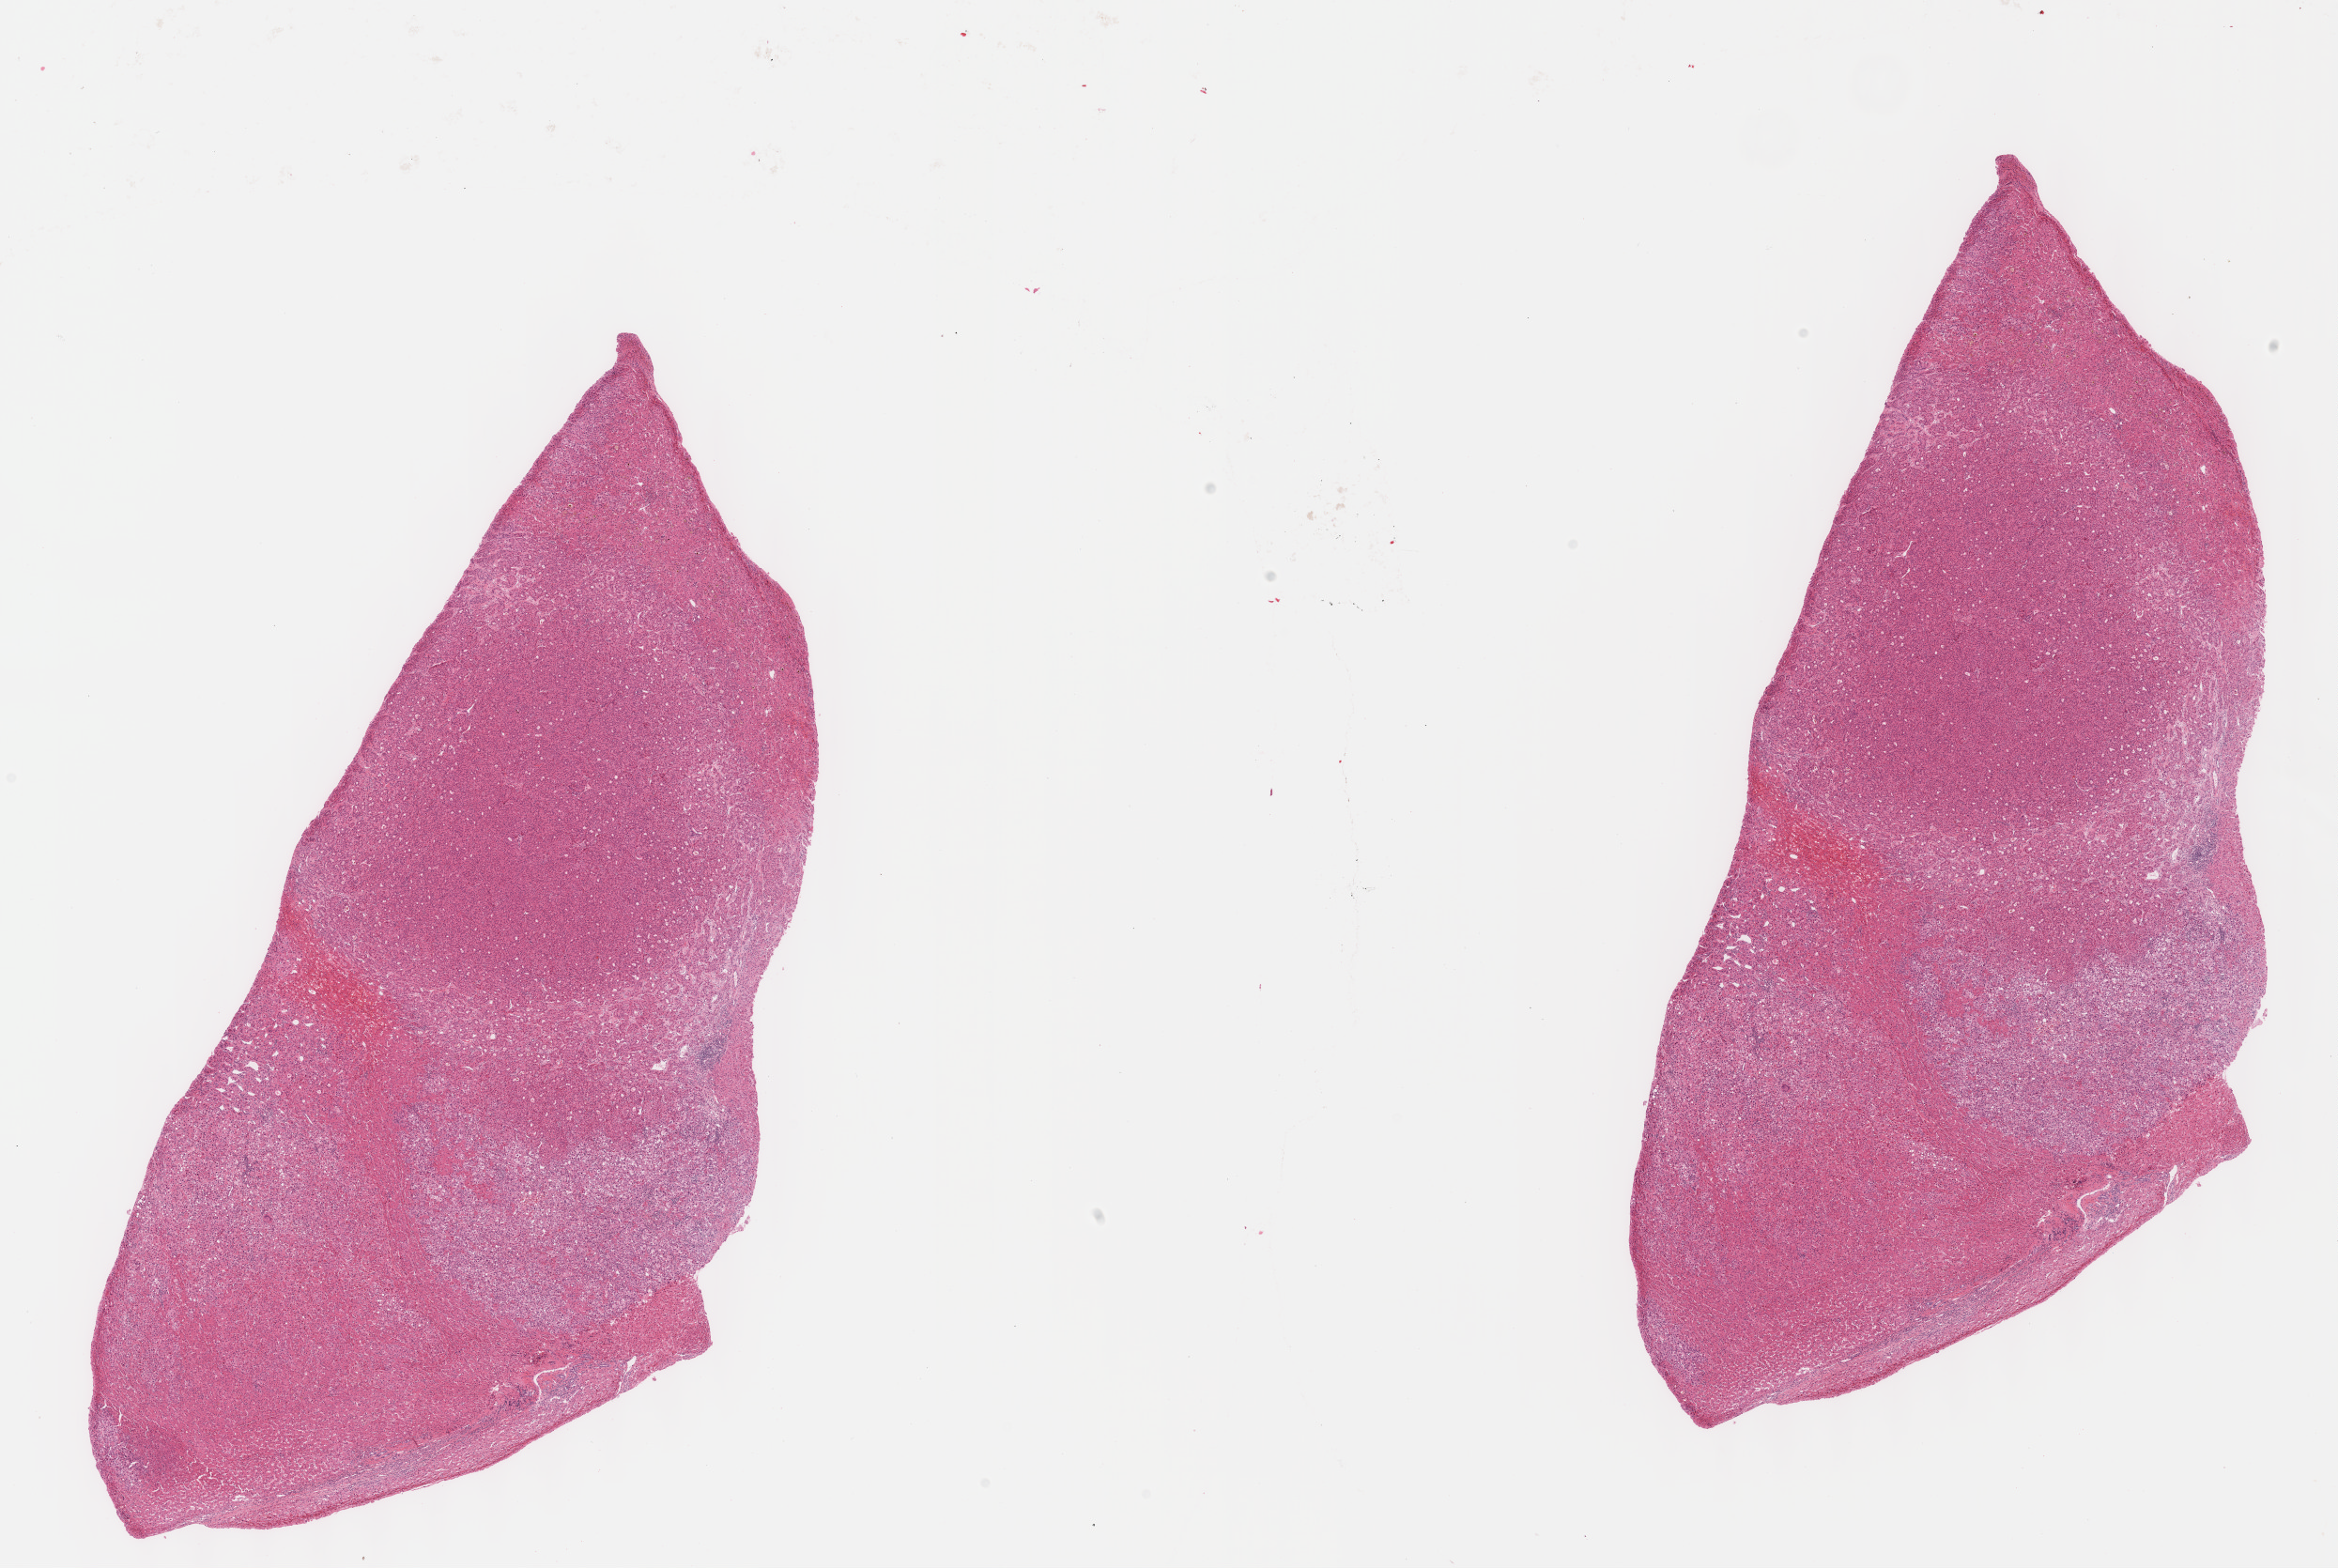
H&E whole-slide image, a low-resolution overview of the entire scanned area, about 20.1 x 13.5 mm, formalin-fixed paraffin-embedded (FFPE) diagnostic section, primary tumour sample from the liver. Patient: male, age at initial diagnosis 45 years. Histologic grade: G3 (poorly differentiated).
- pathologic diagnosis: Hepatocellular carcinoma, NOS
- AJCC pathologic stage: I (7th edition)